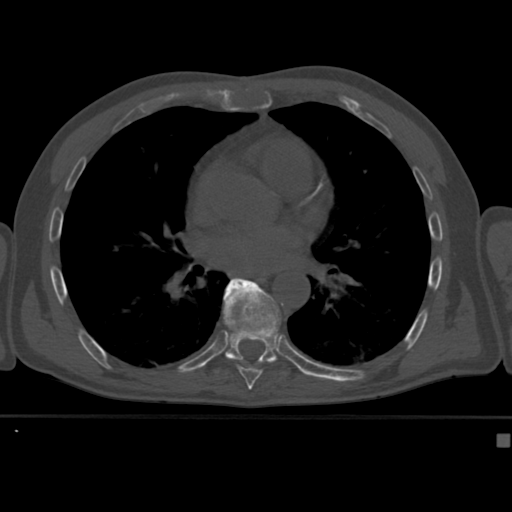
CT including the spine, one axial slice; slice 255 of 430 in the series (ordered by position); reconstruction kernel Br40s; bone window (W 1800 / L 400 HU); 1.5 mm slice thickness; 512 × 512 image matrix, field of view 337 × 337 mm. Male patient, age 64 years. From the clinical record (not read from this slice): primary cancer: uterus.
Structures marked on this image (semi-automatically segmented with operator editing):
- T8 vertebra: bounding box [x1, y1, x2, y2] px = [223, 300, 275, 382]
- T9 vertebra: [216, 278, 285, 375]